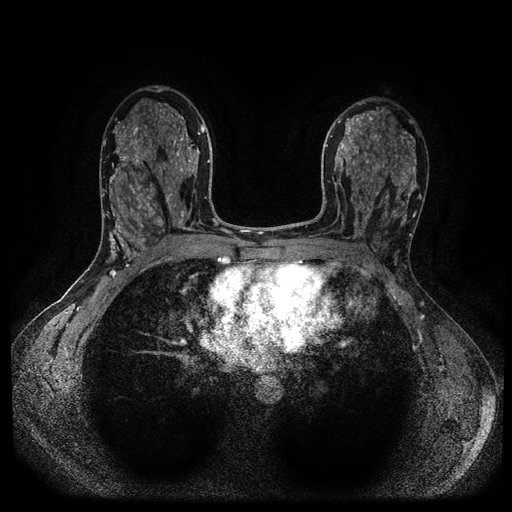
Breast MRI (dynamic contrast-enhanced, multi-phase), one axial slice; position 60 of 116 along the scan axis; dynamic contrast-enhanced series, time point 2 of 5 at this slice position (early post-contrast); 1.5 T; TE 2.6 ms, TR 5.4 ms; 512 × 512 image matrix, field of view 340 × 340 mm. Female patient, age 43 years.
Structures marked on this image (semi-automatic segmentation, software-assisted and operator-edited):
- breast lesion (labelled benign in the annotation): bounding box (x1, y1, x2, y2) in pixels: (154, 216, 166, 229)